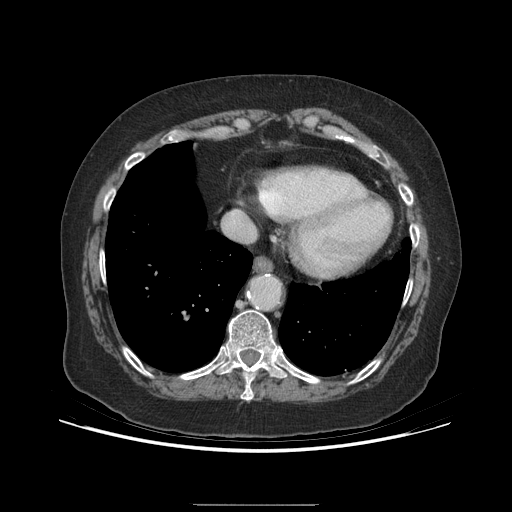
Contrast-enhanced abdominal CT (liver protocol), one axial slice; position 184 of 192 along the scan axis; reconstruction kernel STANDARD; 140 kVp; soft-tissue window (W 400 / L 40 HU); 512 × 512 image matrix, field of view 400 × 400 mm. Case-level facts recorded for this patient, not image findings: diagnosis: hepatocellular carcinoma (patient treated with transarterial chemoembolisation; whether this scan precedes or follows treatment is not stated here); TNM stage (as recorded): Stage-I; Child-Pugh class: A; tumour differentiation: moderately differentiated; tumour size: 3.2 cm.
Annotated regions visible in this slice (semi-automatically segmented with operator editing):
- abdominal aorta: bounding box (x1, y1, x2, y2) in pixels: (251, 277, 279, 308)